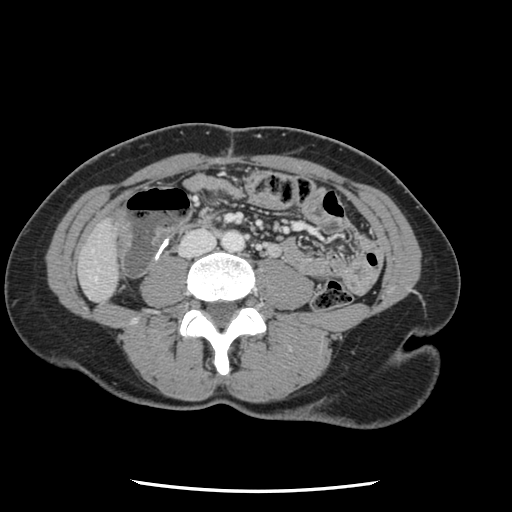
Contrast-enhanced abdominal CT, one axial slice. Position 6 of 134 along the scan axis. Intravenous contrast given. Soft-tissue window (W 400 / L 40 HU). 512 × 512 image matrix, field of view 330 × 330 mm. Female patient, age 43 years. Case-level facts recorded for this patient, not image findings: diagnosis: colorectal cancer liver metastases, imaged before liver resection.
Outlined on this slice (outlined manually by an expert reader):
- liver: bounding box (x1, y1, x2, y2) in pixels: (80, 223, 118, 301)
- planned liver remnant (the part of the liver to remain after resection): (80, 223, 118, 302)